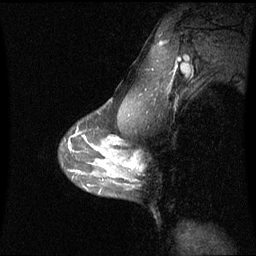
Breast MRI (dynamic contrast-enhanced), one sagittal slice; slice 48 of 60 in the series (ordered by position); dynamic contrast-enhanced series, image 2 of 3 at this slice position (ordered by acquisition); 1.5 T; TE 4.2 ms, TR 8.9 ms; 2 mm slice thickness; 256 × 256 image matrix. Female patient, age 42 years. Case-level facts recorded for this patient, not image findings: setting: breast cancer imaged before/during neoadjuvant chemotherapy; receptor status: triple-negative.
Structures marked on this image (semi-automatic segmentation, software-assisted and operator-edited):
- analysis volume of interest (the breast-tissue region the enhancement analysis was run in; not a lesion): box from (x=114, y=150) to (x=137, y=180) px
- tumour enhancement mask (voxels above the 70 % enhancement threshold inside the analysis volume of interest): (x=127, y=159)–(x=136, y=170)